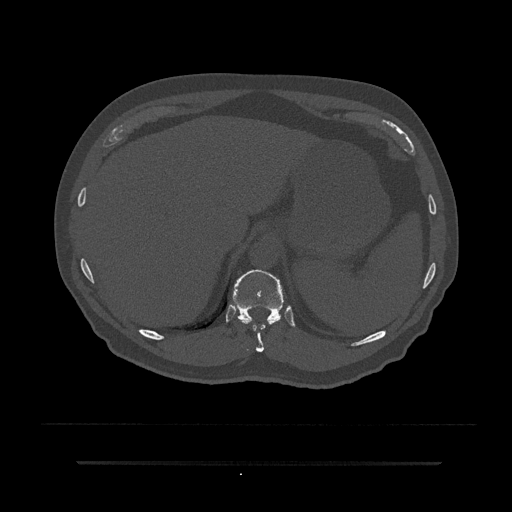
CT including the spine, one axial slice; slice 294 of 797 in the series (ordered by position); reconstruction kernel Br40s/3; 120 kVp; bone window (W 1800 / L 400 HU); 512 × 512 image matrix, field of view 464 × 464 mm. Male patient, age 59 years. Case-level facts recorded for this patient, not image findings: primary cancer: bile ducts; vertebrae with lytic lesions (as recorded): T10.
Outlined on this slice (semi-automatically segmented with operator editing):
- T10 vertebra: box from (x=234, y=278) to (x=280, y=352) px
- T11 vertebra: (x=229, y=269)–(x=287, y=323)